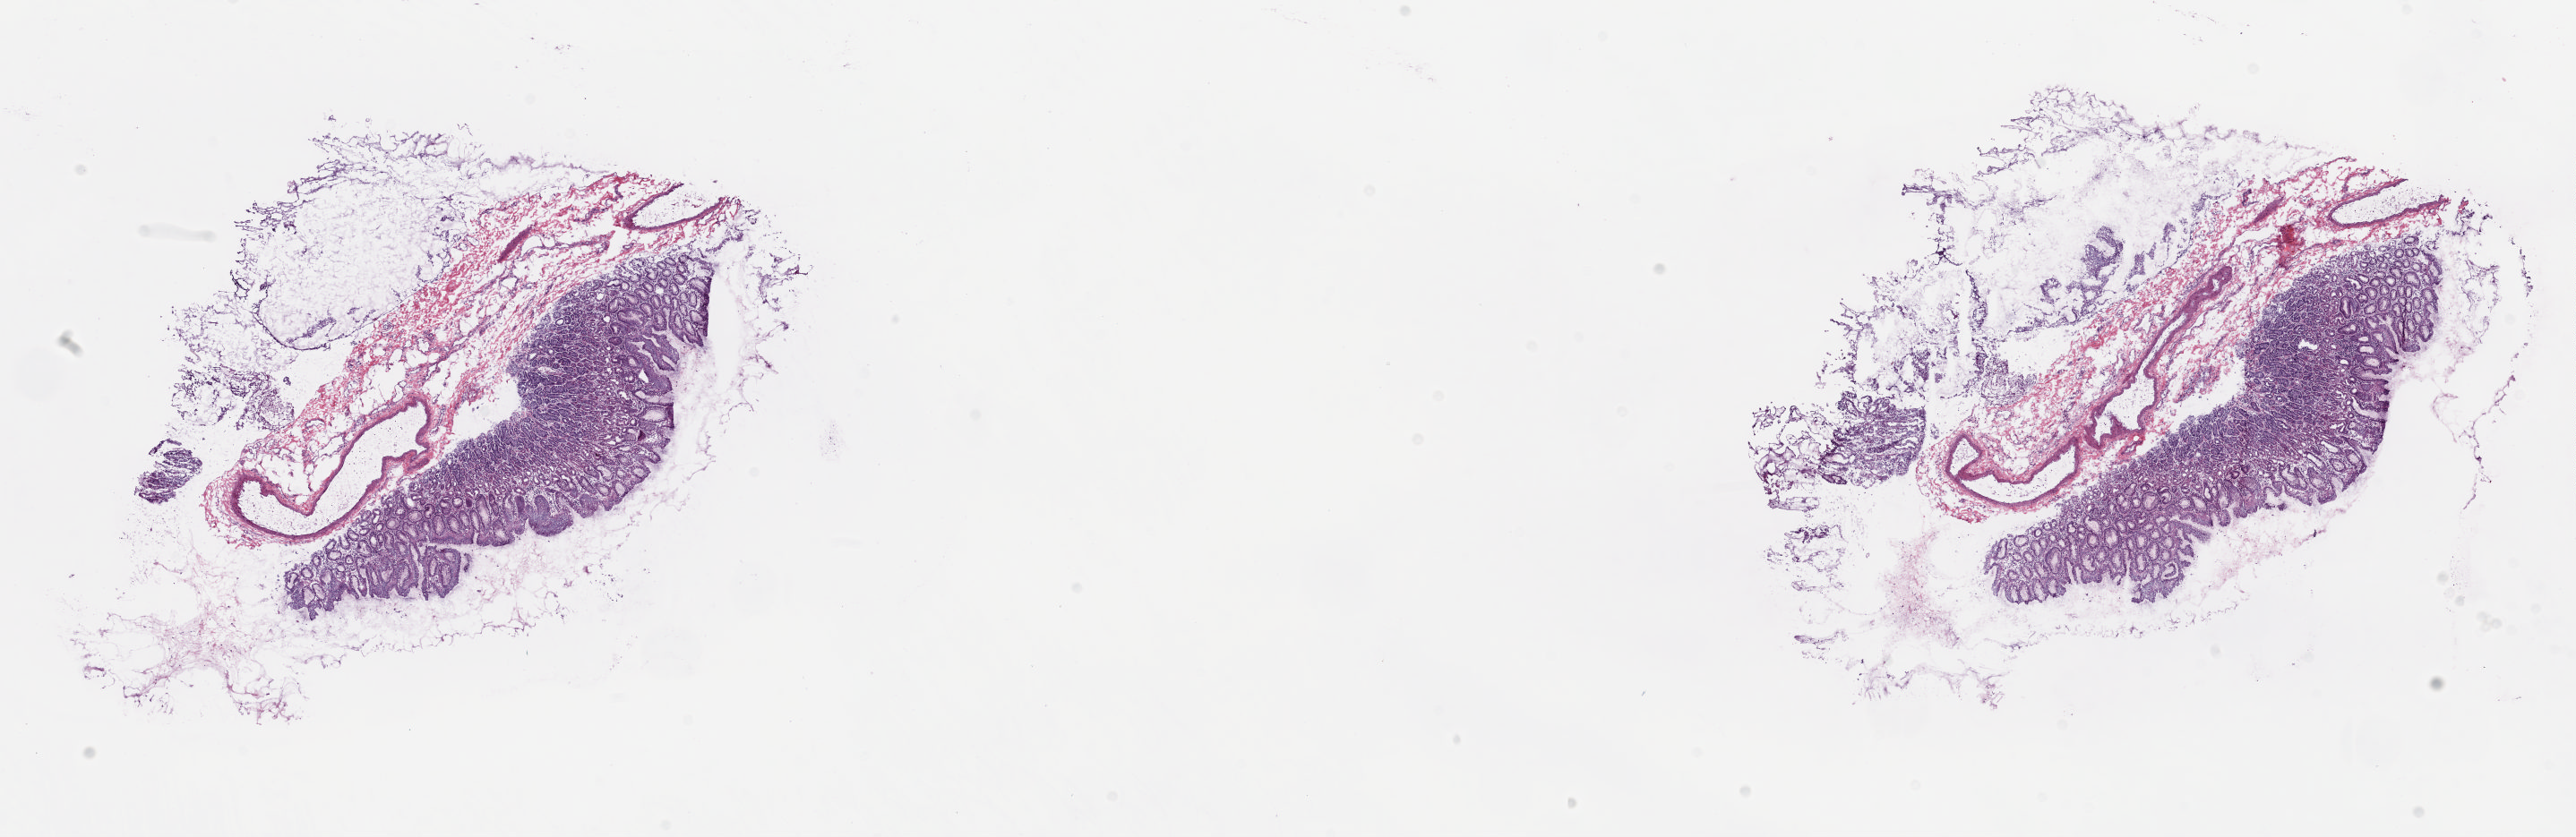
Whole-slide histology image, H&E-stained — a low-resolution overview of the entire scanned area, about 22.8 x 7.4 mm (from a 20x scan), frozen section from the top of the tissue portion, esophagus, solid tissue normal (non-tumour tissue) sample. Patient: male, age at initial diagnosis 54 years. Slide review estimates, as recorded: tumour cells 0%, tumour nuclei 0%, normal cells 100%, stromal cells 0%, necrosis 0%. Infiltration values recorded for this section: lymphocyte infiltration 2%, monocyte infiltration 2%, neutrophil infiltration 0%.
• this section: solid tissue normal sample (biorepository sample class)
• patient diagnosis: Adenocarcinoma, NOS